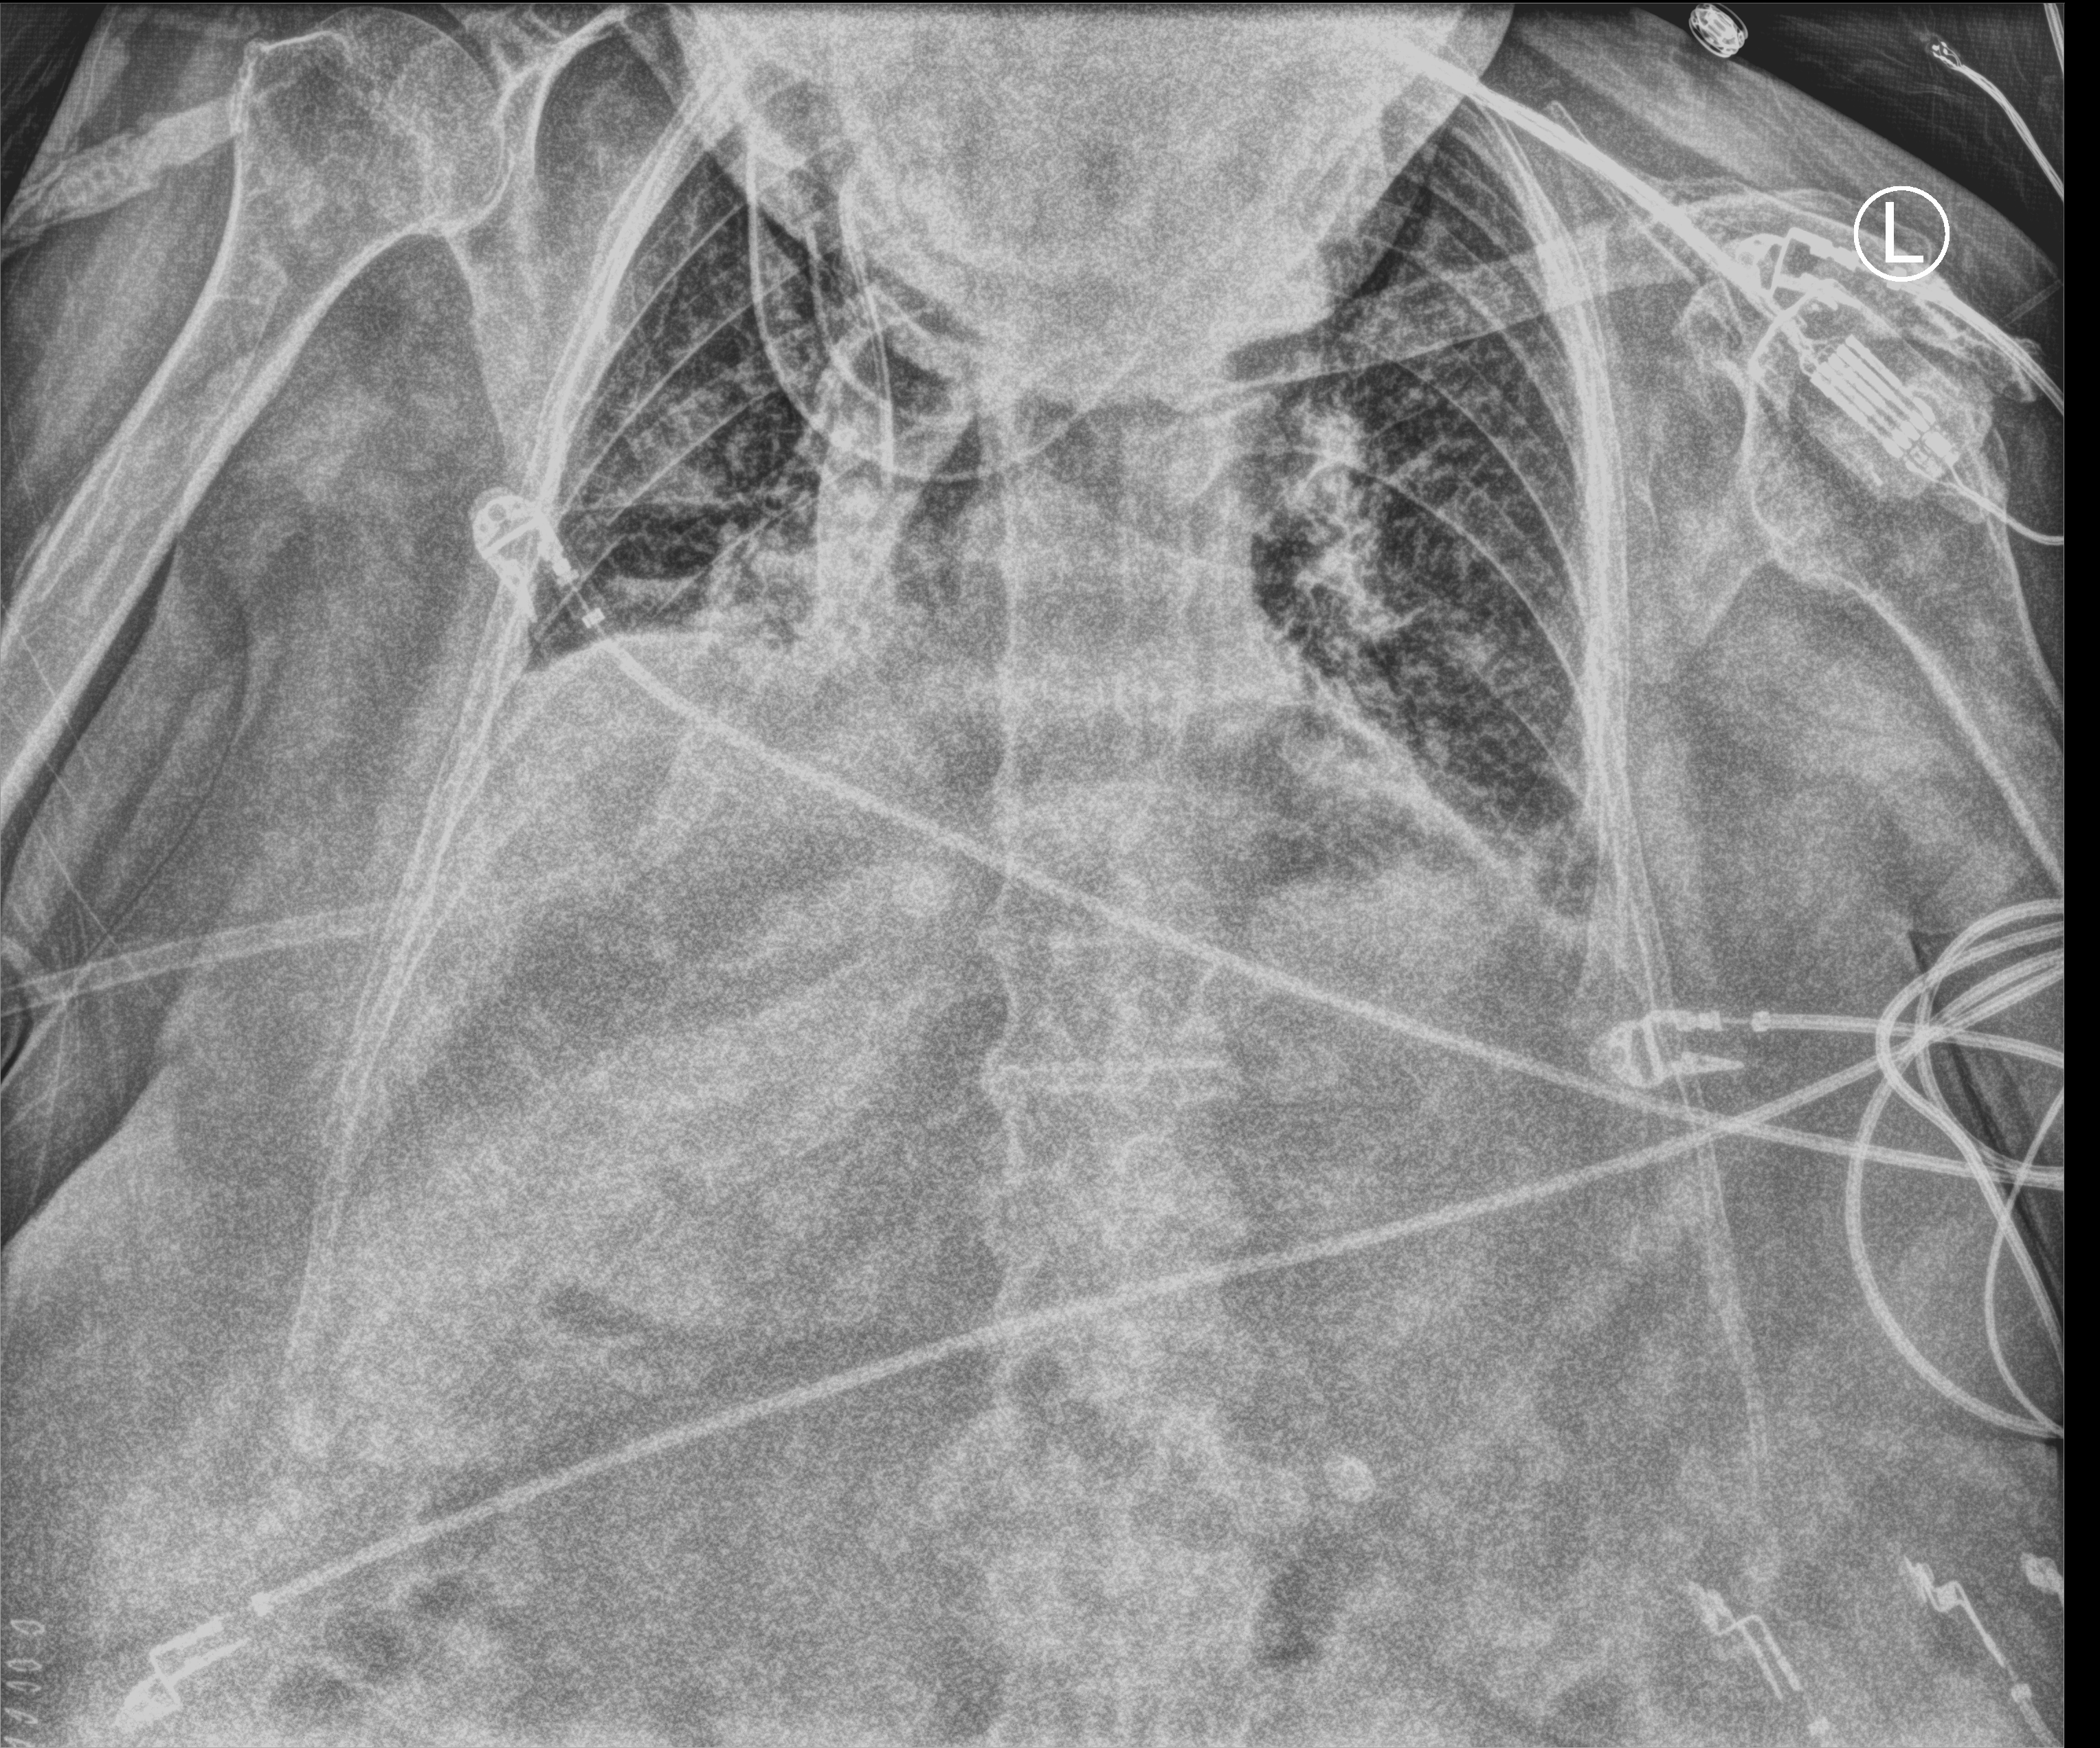
Portable chest radiograph; anteroposterior (AP) projection. Female patient hospitalised with COVID-19, age 75–90 years.
Admission-level facts for this patient (not findings on this image; timing relative to this image not recorded):
- mechanically ventilated during this hospital stay: yes